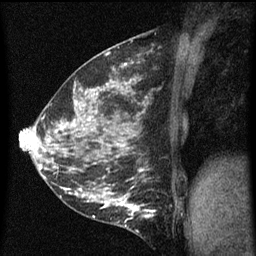
Breast MRI (dynamic contrast-enhanced), one sagittal slice; position 23 of 60 along the scan axis; dynamic contrast-enhanced series, image 2 of 5 at this slice position (ordered by acquisition); 1.5 T; TE 4.2 ms, TR 8 ms; 2 mm slice thickness; 256 × 256 image matrix, field of view 180 × 180 mm. Female patient, age 35 years.
Structures marked on this image (semi-automatic segmentation, software-assisted and operator-edited):
- analysis volume of interest (the breast-tissue region the enhancement analysis was run in; not a lesion): bounding box [x1, y1, x2, y2] px = [118, 194, 157, 229]
- tumour enhancement mask (voxels above the 70 % enhancement threshold inside the analysis volume of interest): [120, 198, 156, 227]